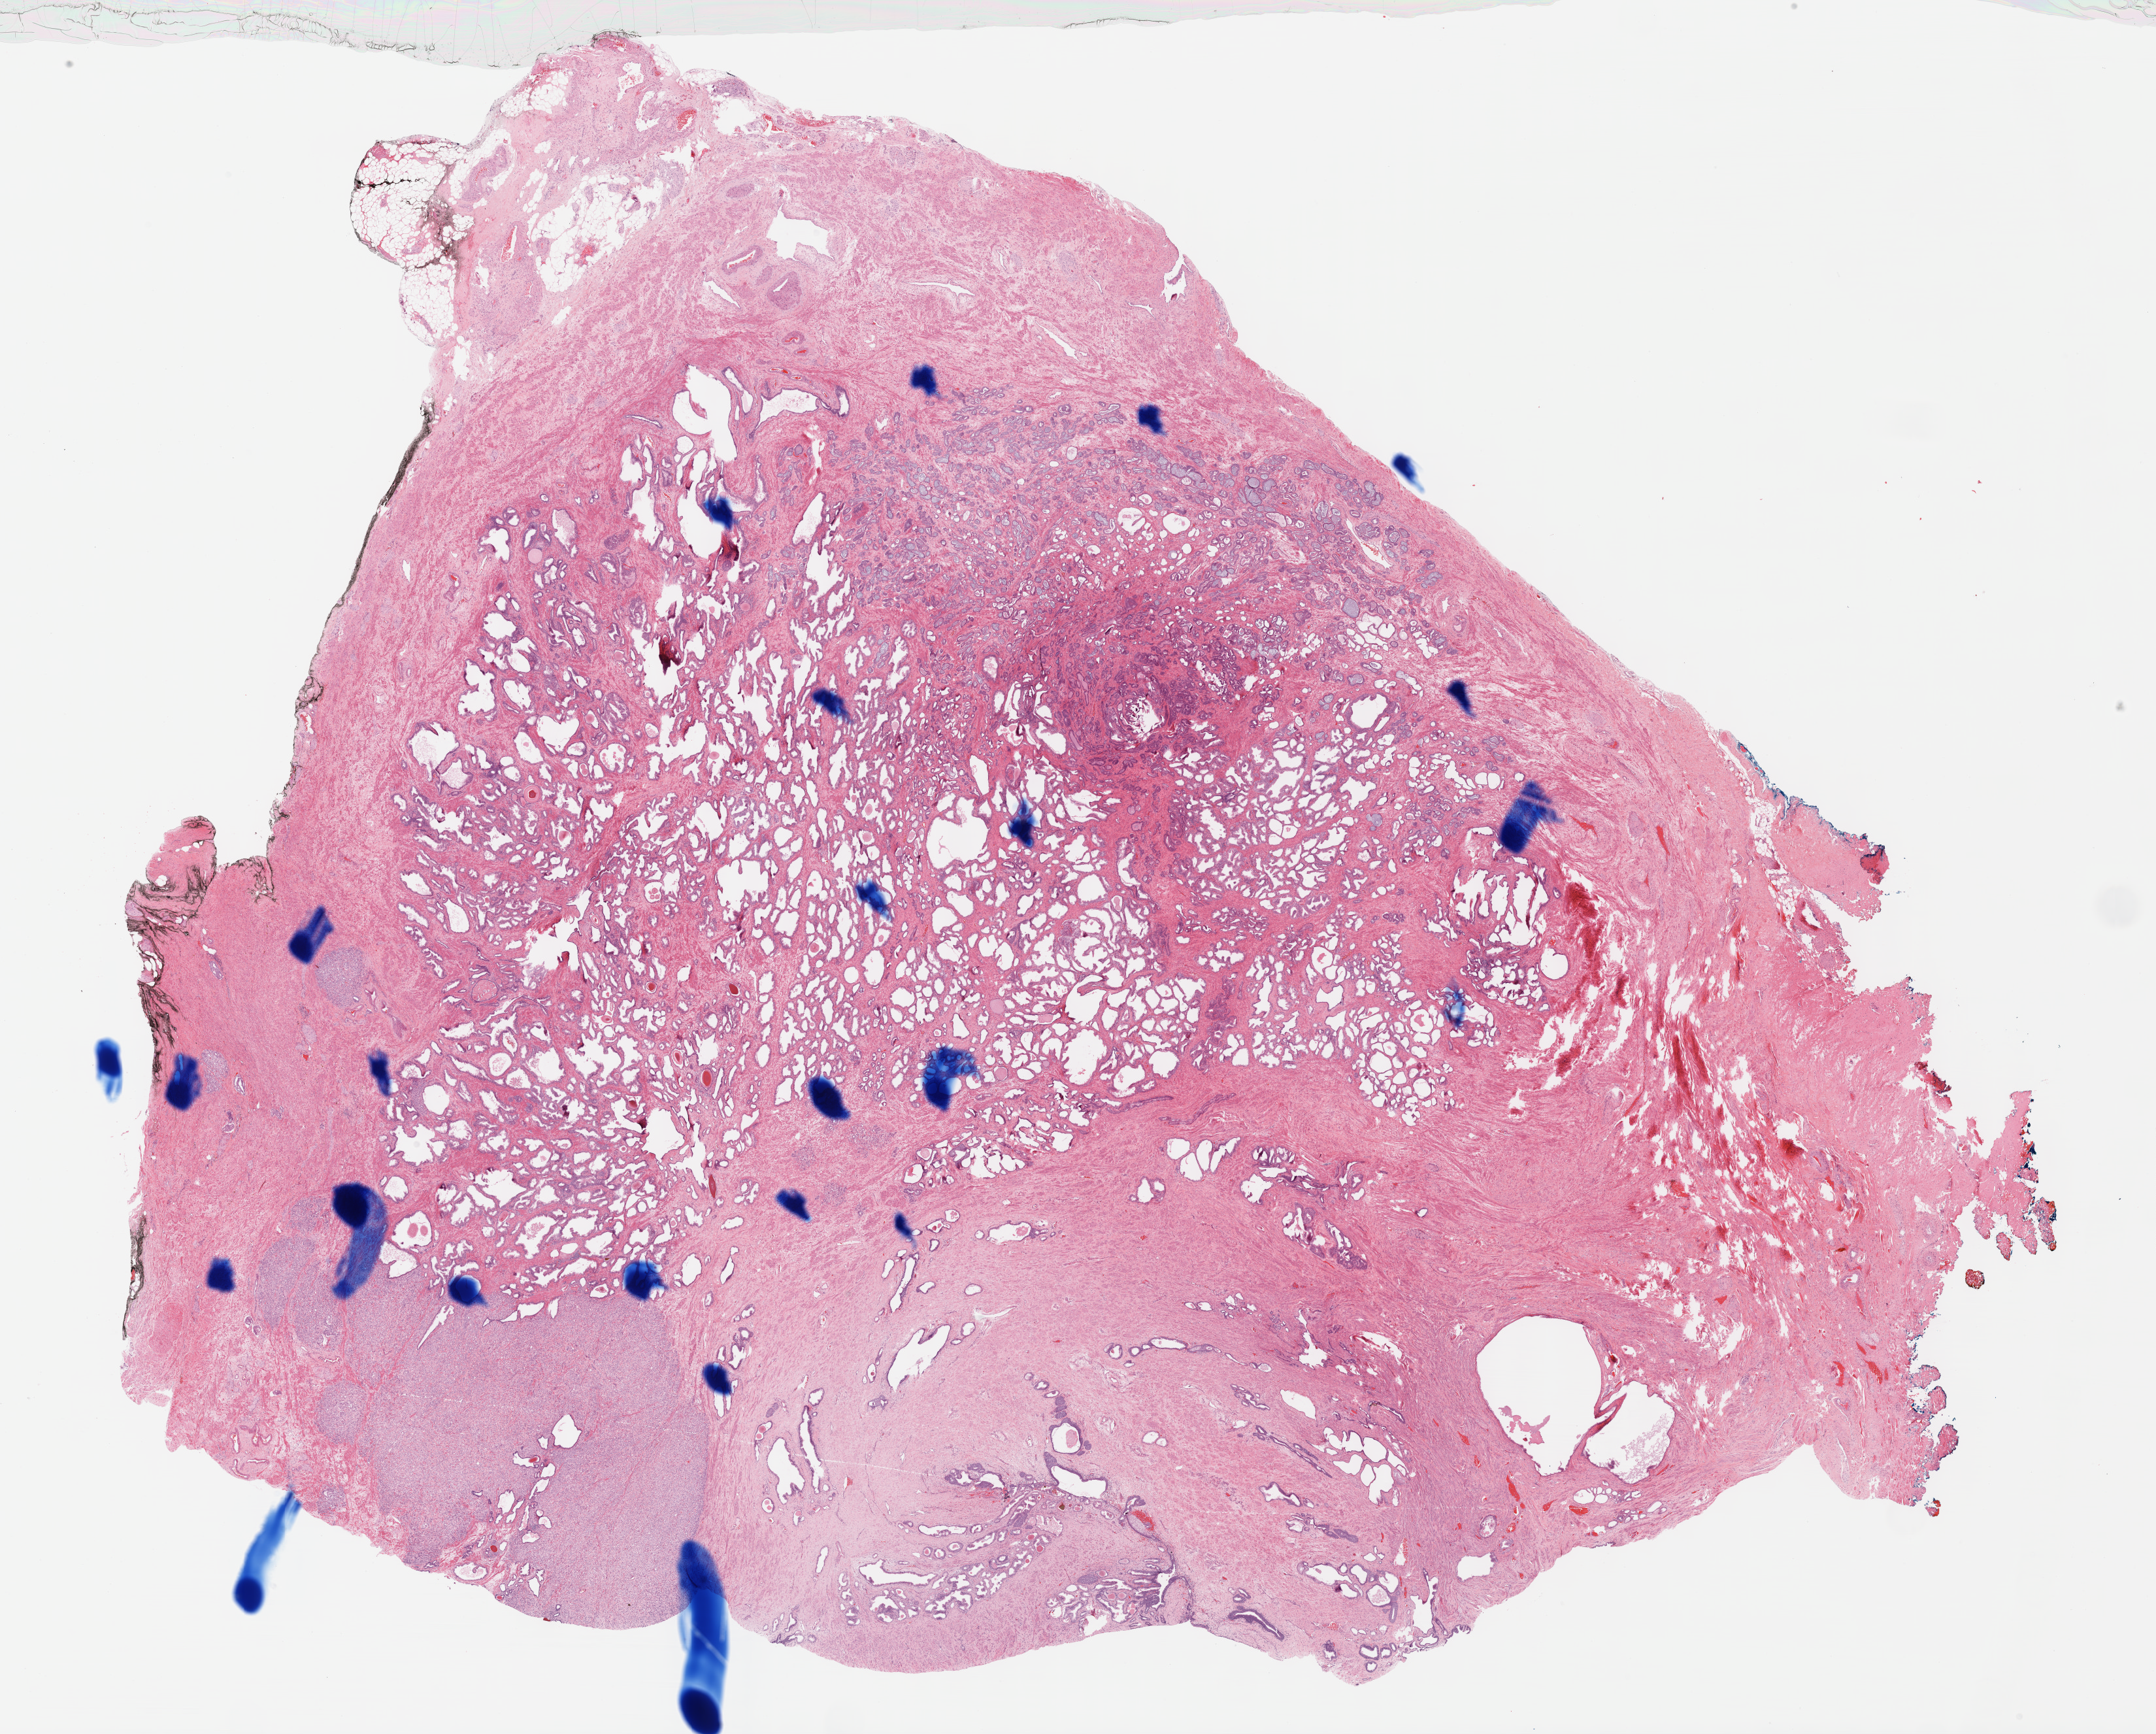
H&E-stained whole-slide image — a low-resolution overview of the entire scanned area, about 26.7 x 21.5 mm (acquisition: 40x scan); formalin-fixed paraffin-embedded (FFPE) diagnostic section; sample: primary tumour, prostate. Male, age 63 years at initial diagnosis. Gleason score: 8 (4+4).
* laterality: right
* diagnosis: Adenocarcinoma, NOS (prostate gland)